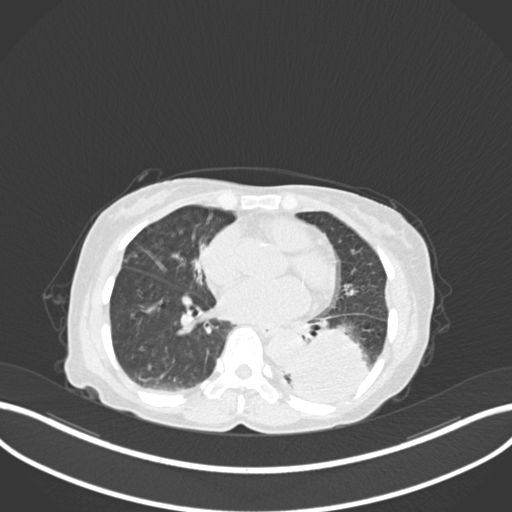
Chest CT, one axial slice; slice 60 of 233 in the series (ordered by position); lung window (W 1500 / L -600 HU); 1 mm slice thickness; 512 × 512 image matrix. Female patient, age 78 years. From the clinical record (not read from this slice): clinical TNM (as recorded): T3 N0 M1.
Annotated regions visible in this slice (bounding box drawn by a radiologist):
- lung tumour (recorded histology: squamous cell carcinoma): bounding box <292,325,370,409> (left, top, right, bottom; pixels)